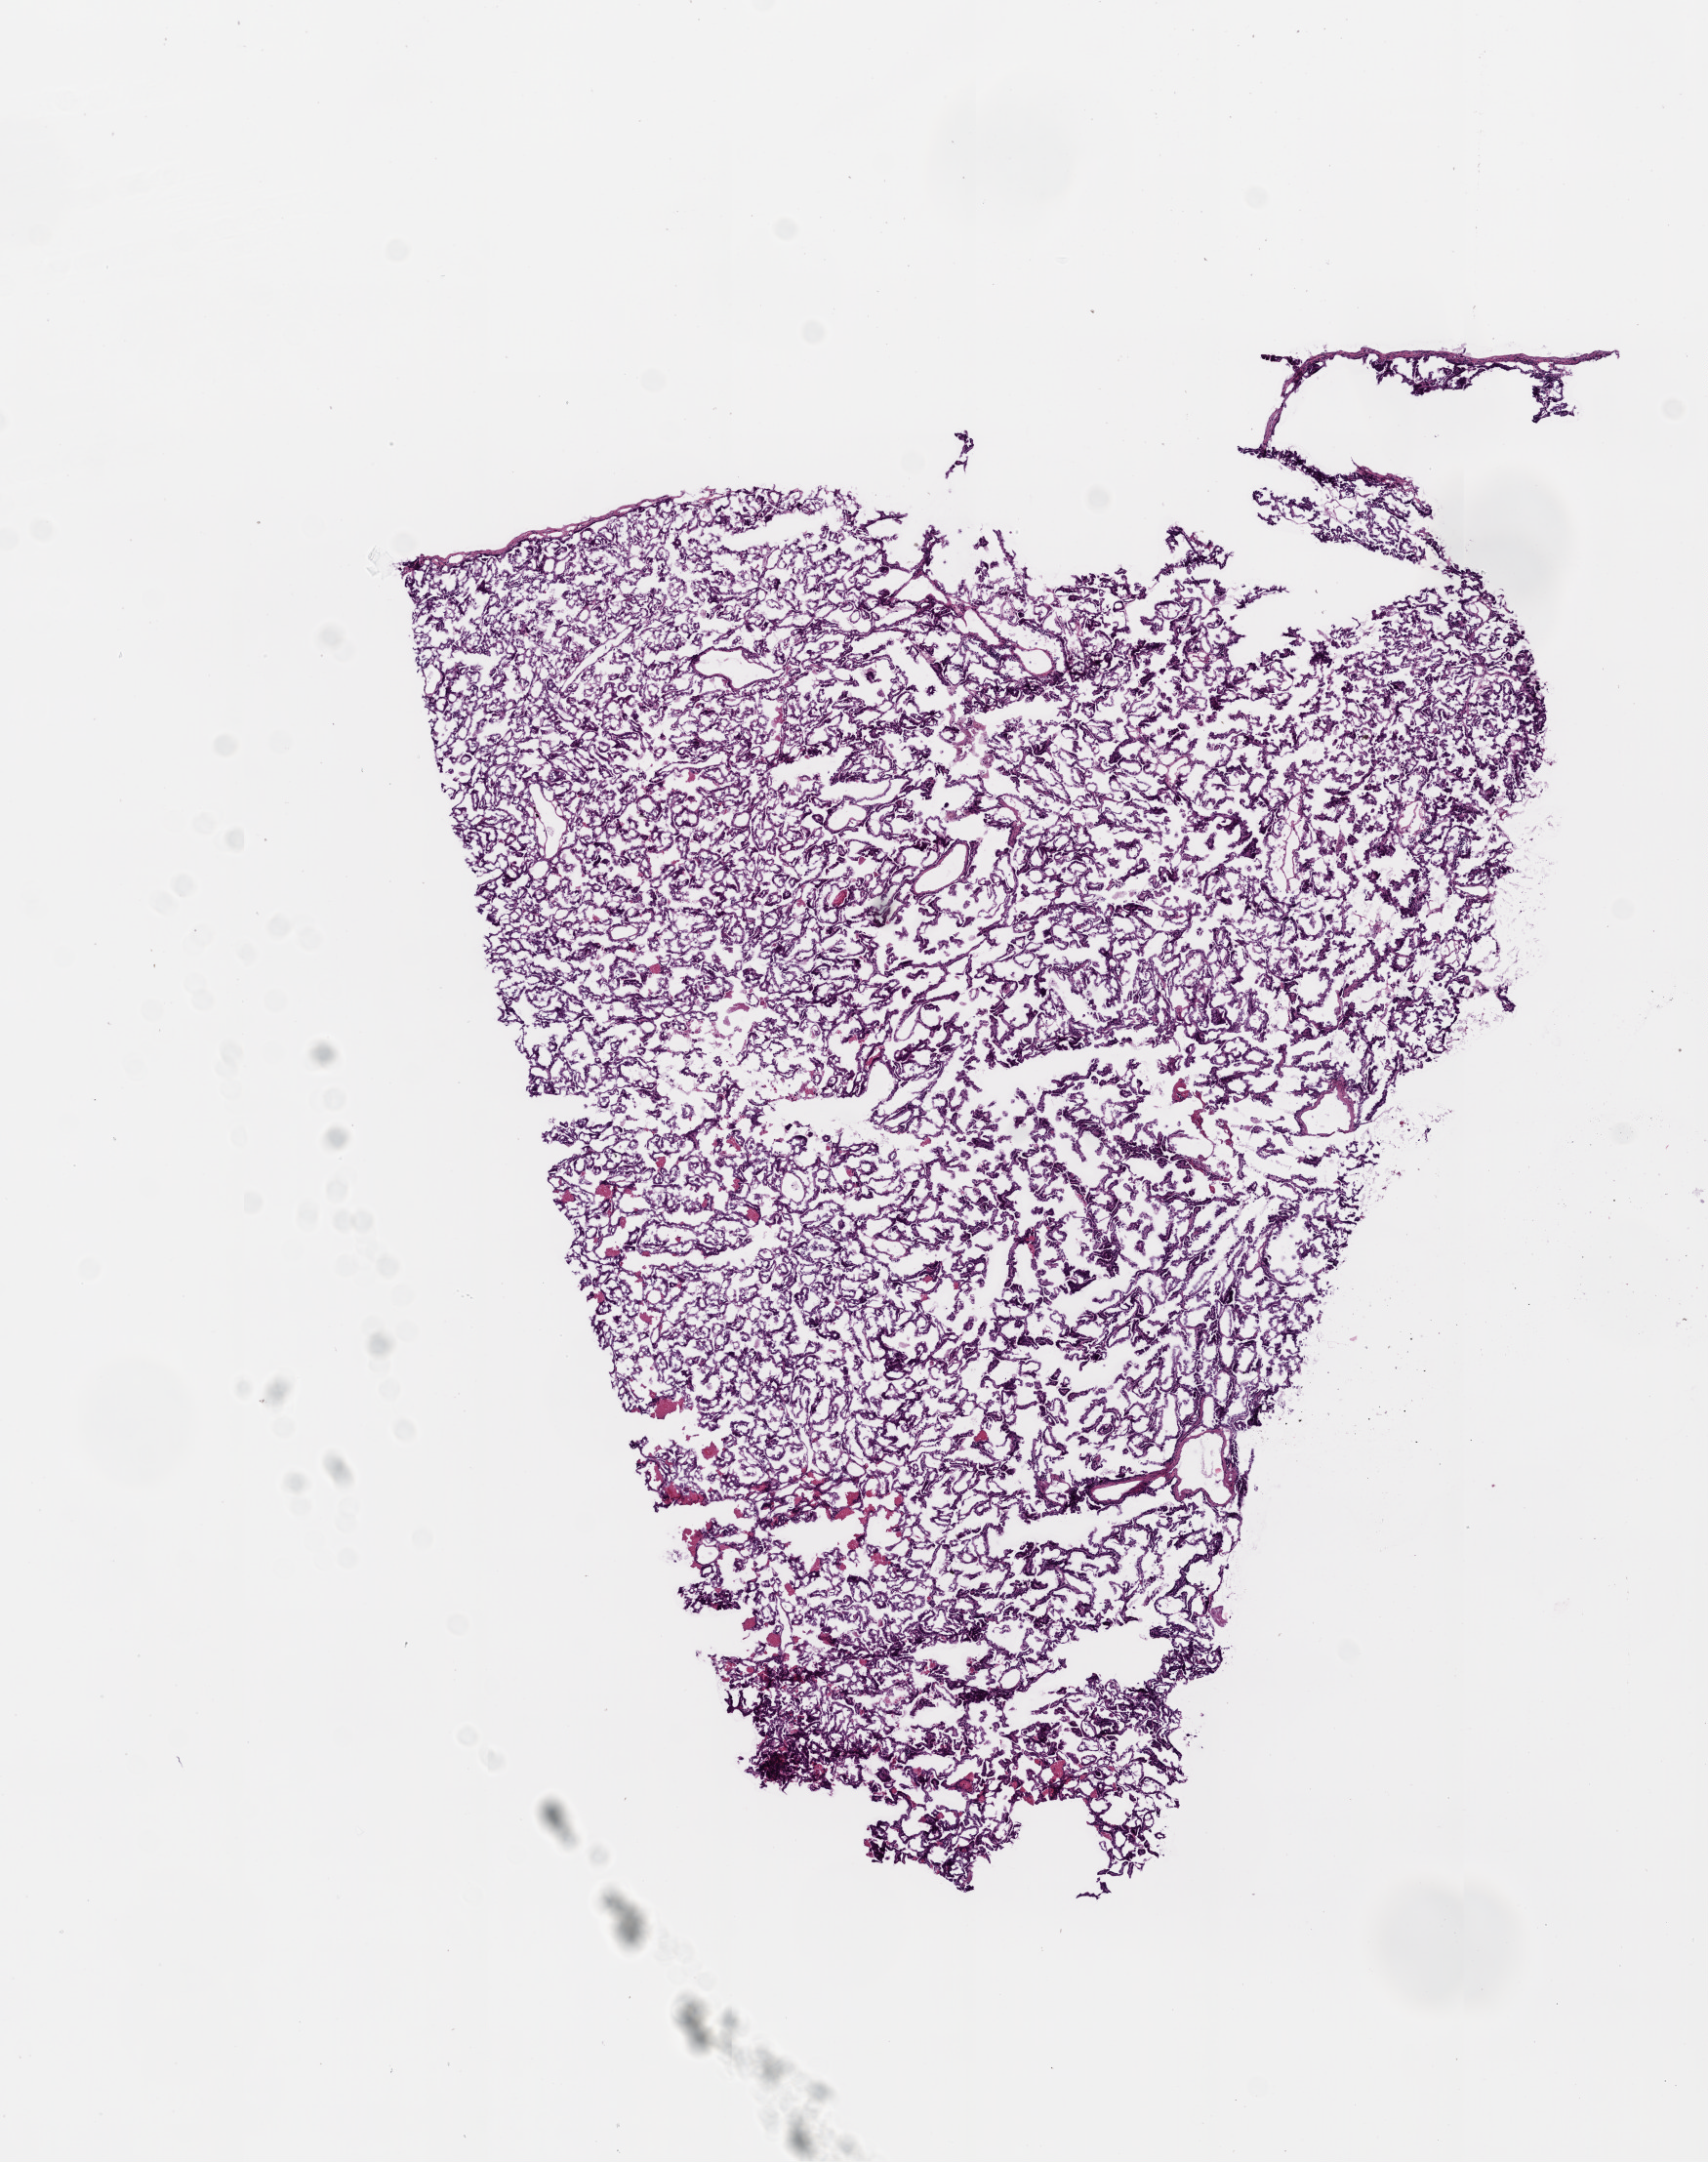
H&E whole-slide image — shown as a low-resolution overview of the whole scanned area (about 7.0 x 8.9 mm), frozen section, primary tumour sample from the lung. Male patient; age at initial diagnosis 72 years. Slide review estimates, as recorded: tumour cells 94%, tumour nuclei 75%, normal cells 0%, stromal cells 5%, necrosis 1%.
* TNM: T1 N0 M0
* AJCC pathologic stage: IA (3rd edition)
* laterality: right
* diagnosis: Adenocarcinoma, NOS (lower lobe, lung)